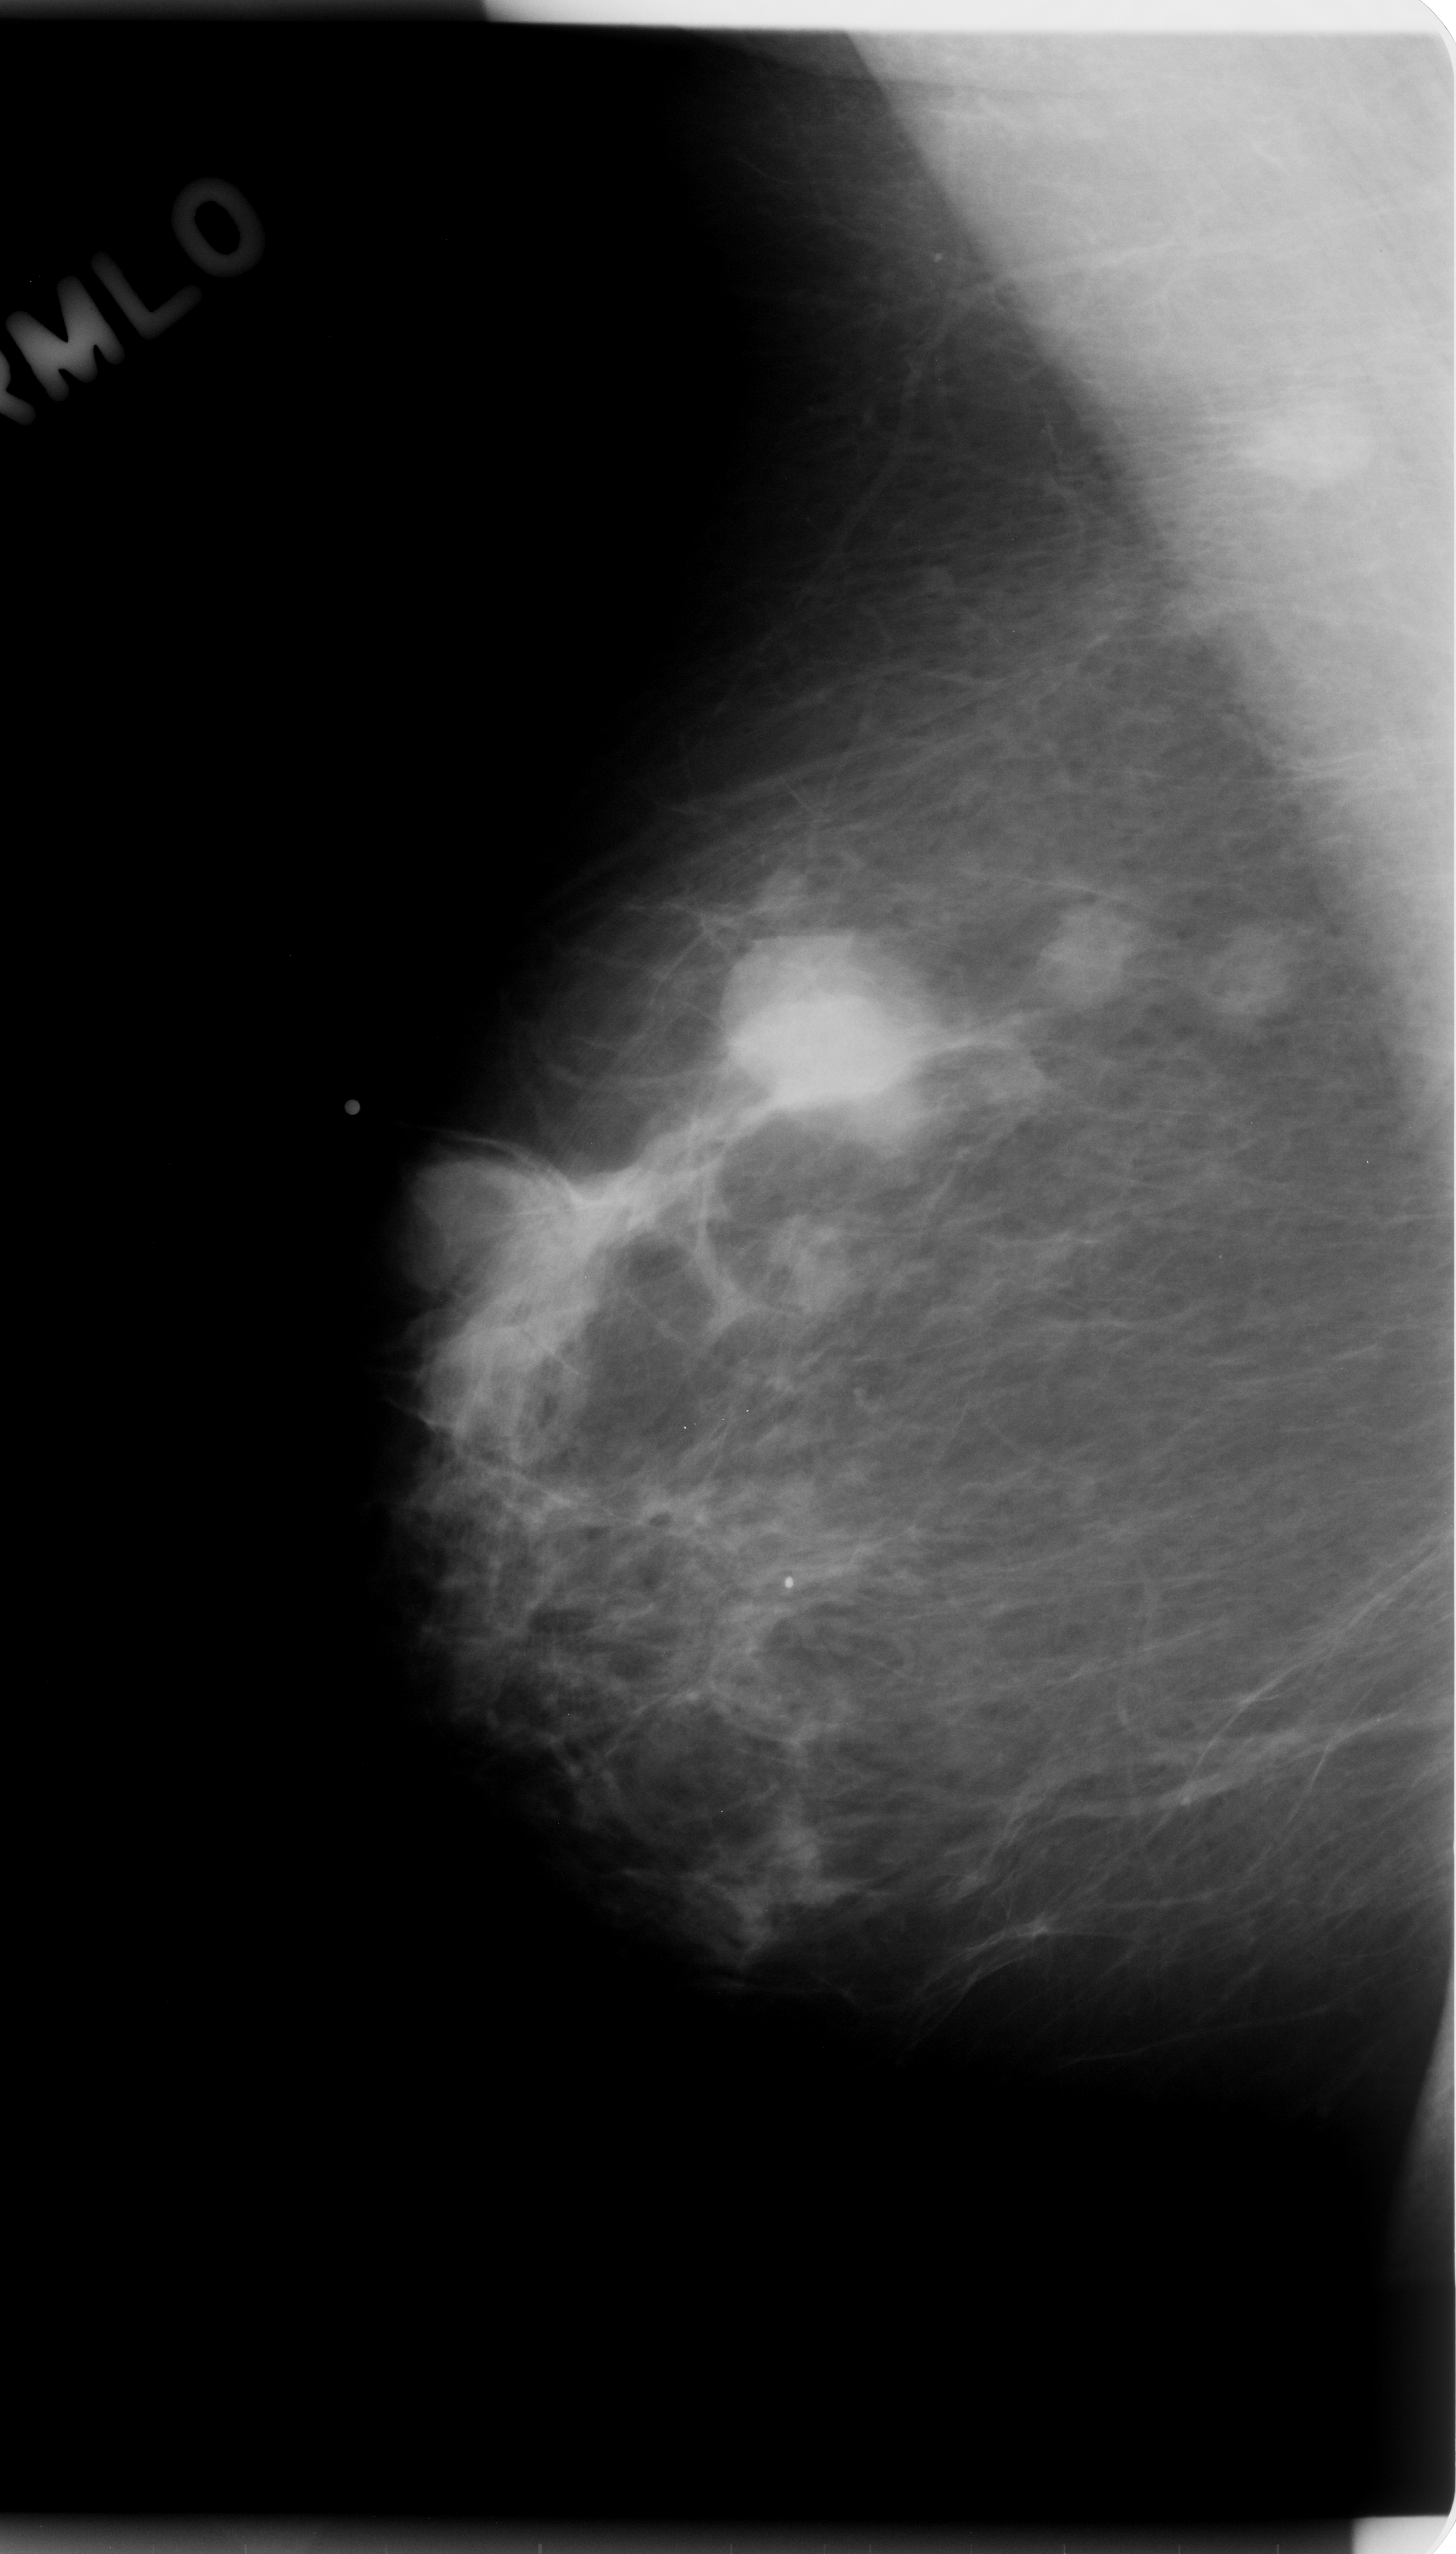
Scanned film-screen mammogram; right breast; mediolateral oblique (MLO) view; BI-RADS breast density category 1 (scale 1–4); 1456 × 2554 image matrix.
Expert-marked regions of interest on this image (one box per marked abnormality):
- mass, shape lobulated, margins circumscribed; BI-RADS assessment category 5; subtlety rating 5 on a 1 (subtle) to 5 (obvious) scale; pathology (as recorded): malignant: bounding box [x1, y1, x2, y2] px = [676, 932, 984, 1144]